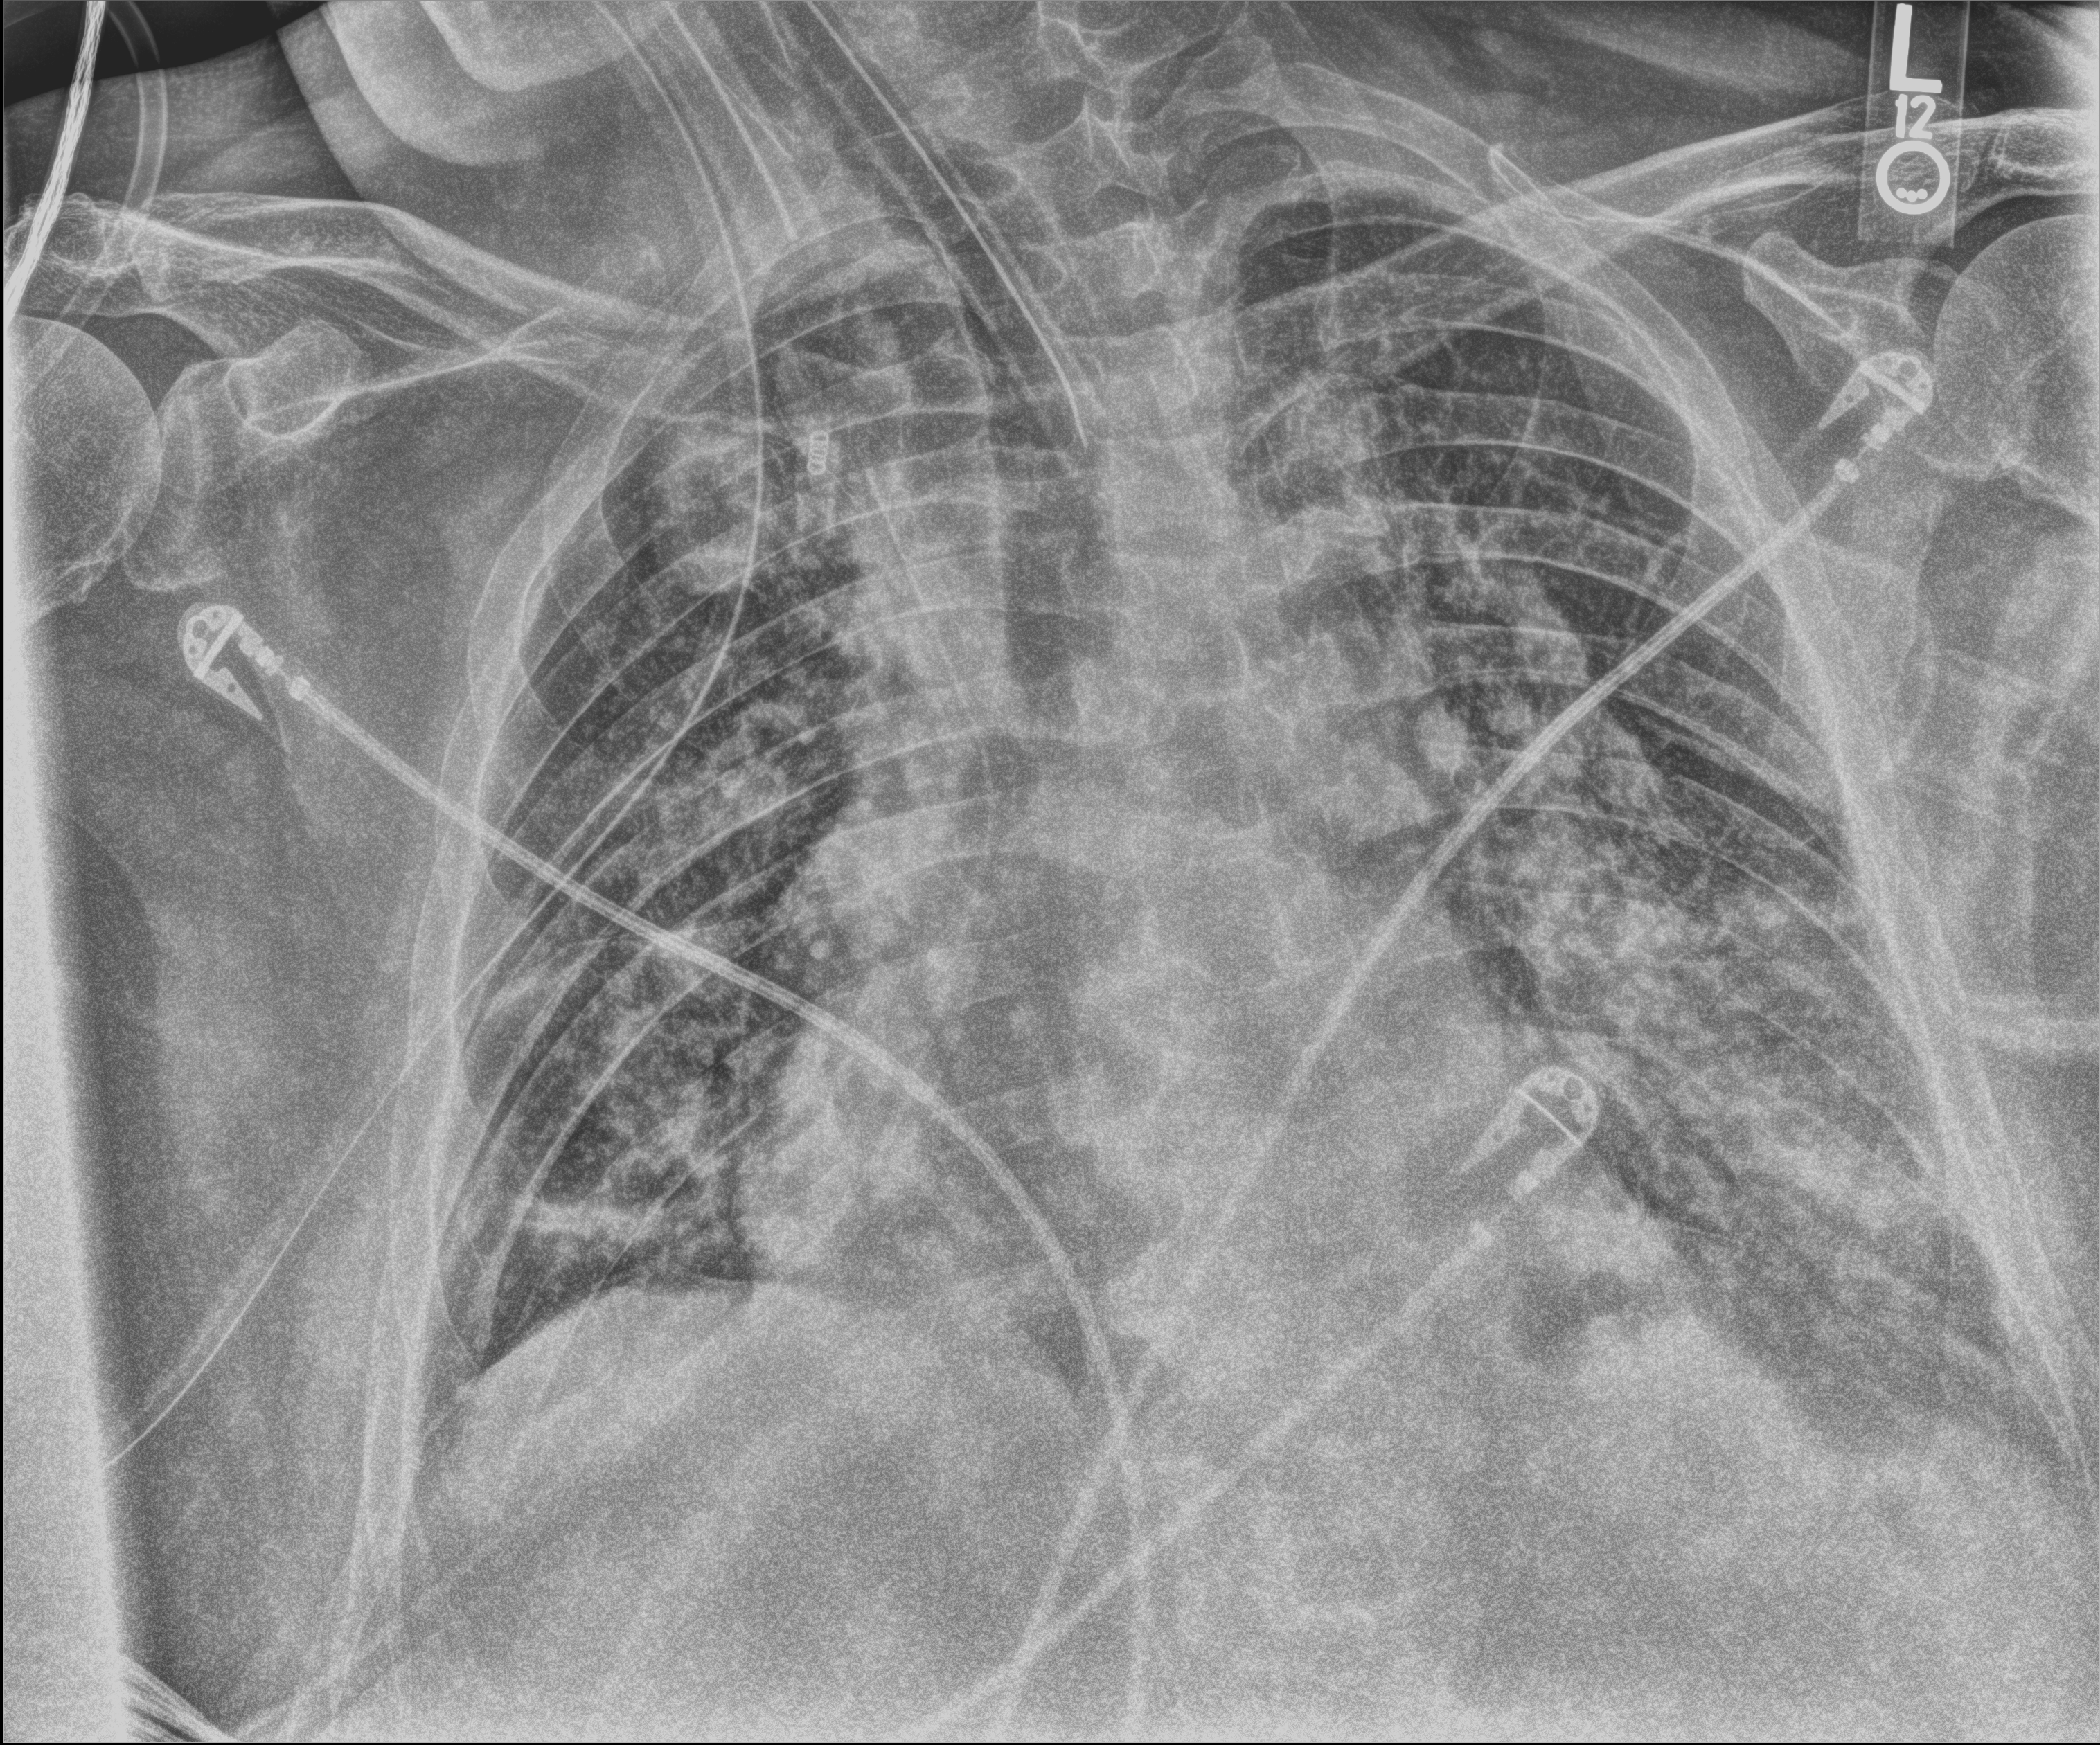
Chest X-ray, anteroposterior (AP) projection. Patient hospitalised with COVID-19; male, aged 60–74 years.
Hospital-stay facts (about this admission, not read from this image; timing relative to this image not recorded): other chronic lung disease (admission record): yes; diabetes (admission record): no; length of hospital stay: 10 days.